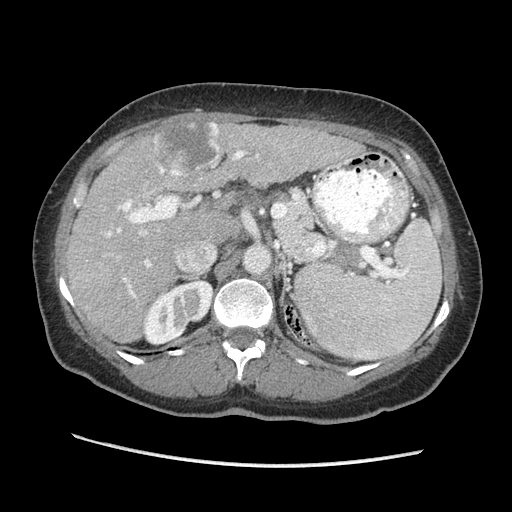
Contrast-enhanced abdominal CT (liver protocol), one axial slice. Slice 131 of 170 in the series (ordered by position). 140 kVp. Soft-tissue window (W 400 / L 40 HU). 2.5 mm slice thickness. 512 × 512 image matrix. From the clinical record (not read from this slice): diagnosis: hepatocellular carcinoma (patient treated with transarterial chemoembolisation; whether this scan precedes or follows treatment is not stated here); TNM stage (as recorded): Stage-II; Child-Pugh class: A; tumour differentiation: no biopsy.
Annotated regions visible in this slice (semi-automatic segmentation, software-assisted and operator-edited):
- liver parenchyma outside the tumour (the mass and vessels are separate outlines, so this box may not span the whole liver): box from (x=66, y=122) to (x=364, y=342) px
- mass: (x=152, y=117)–(x=222, y=177)
- liver vessels: (x=105, y=150)–(x=350, y=298)